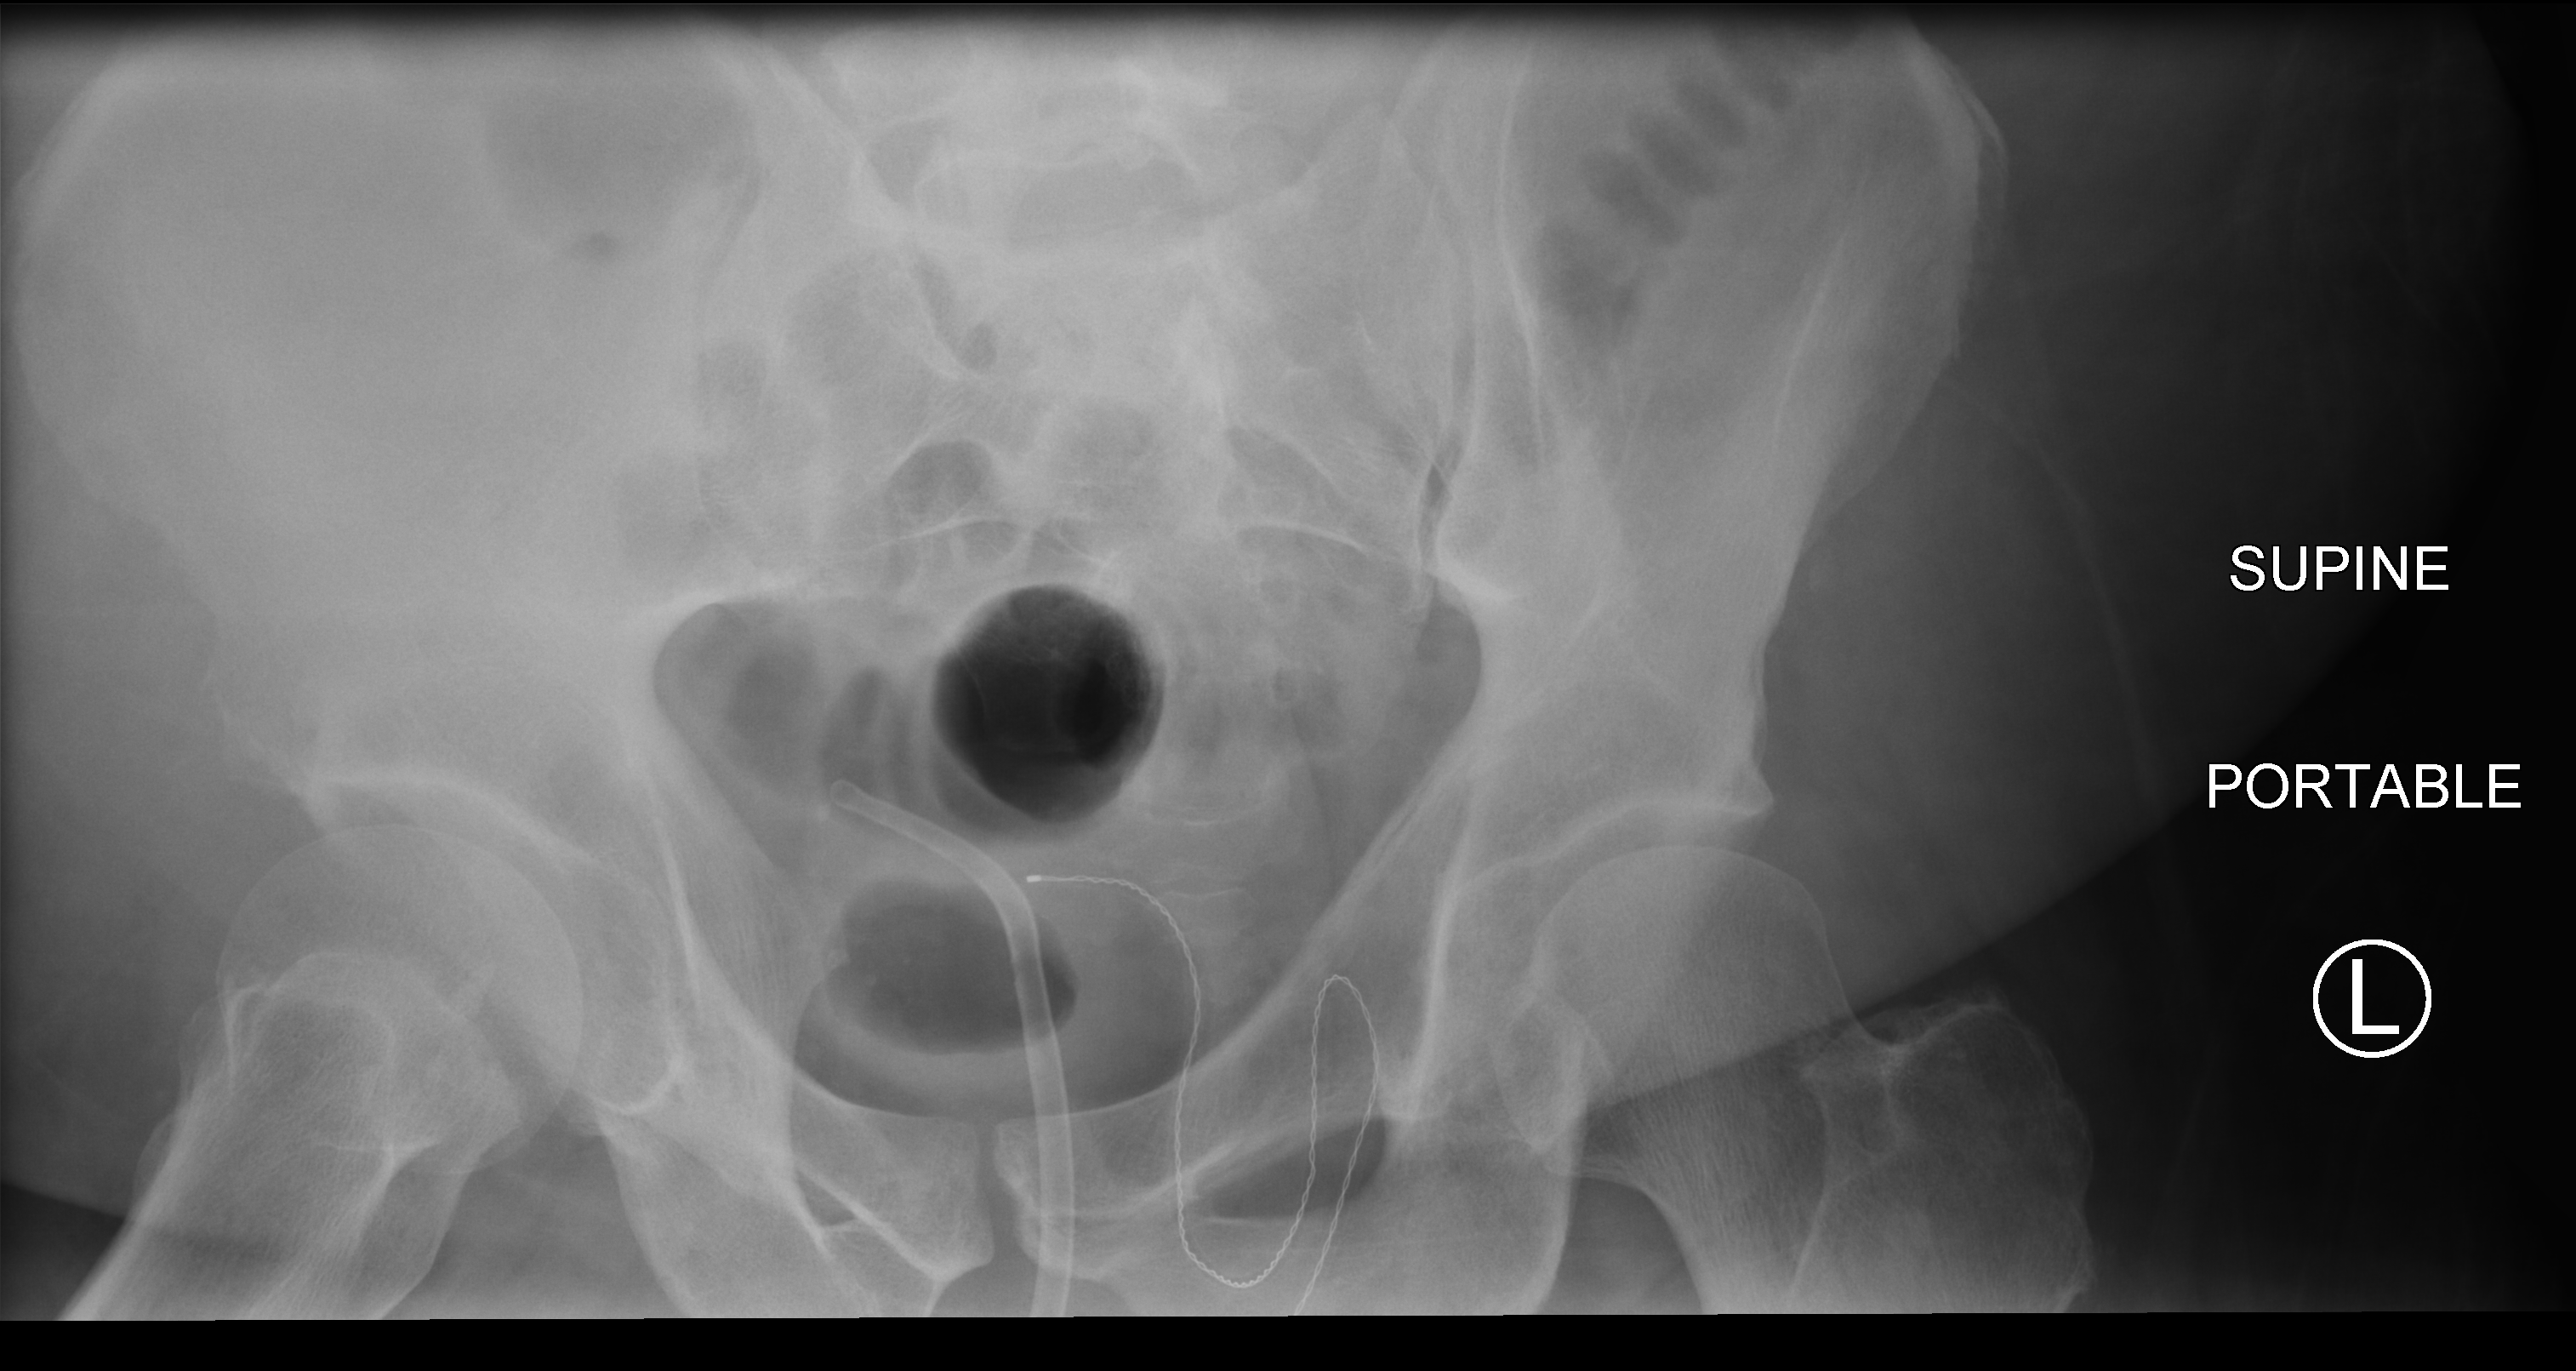
Portable abdomen radiograph; anteroposterior (AP) projection. Patient hospitalised with COVID-19; male, aged 18–59 years.
From the hospital-stay record, not from the radiograph (when in the stay this image was taken is not recorded):
- length of hospital stay: 28 days
- mechanically ventilated during this hospital stay: yes
- admitted to intensive care during this hospital stay: yes